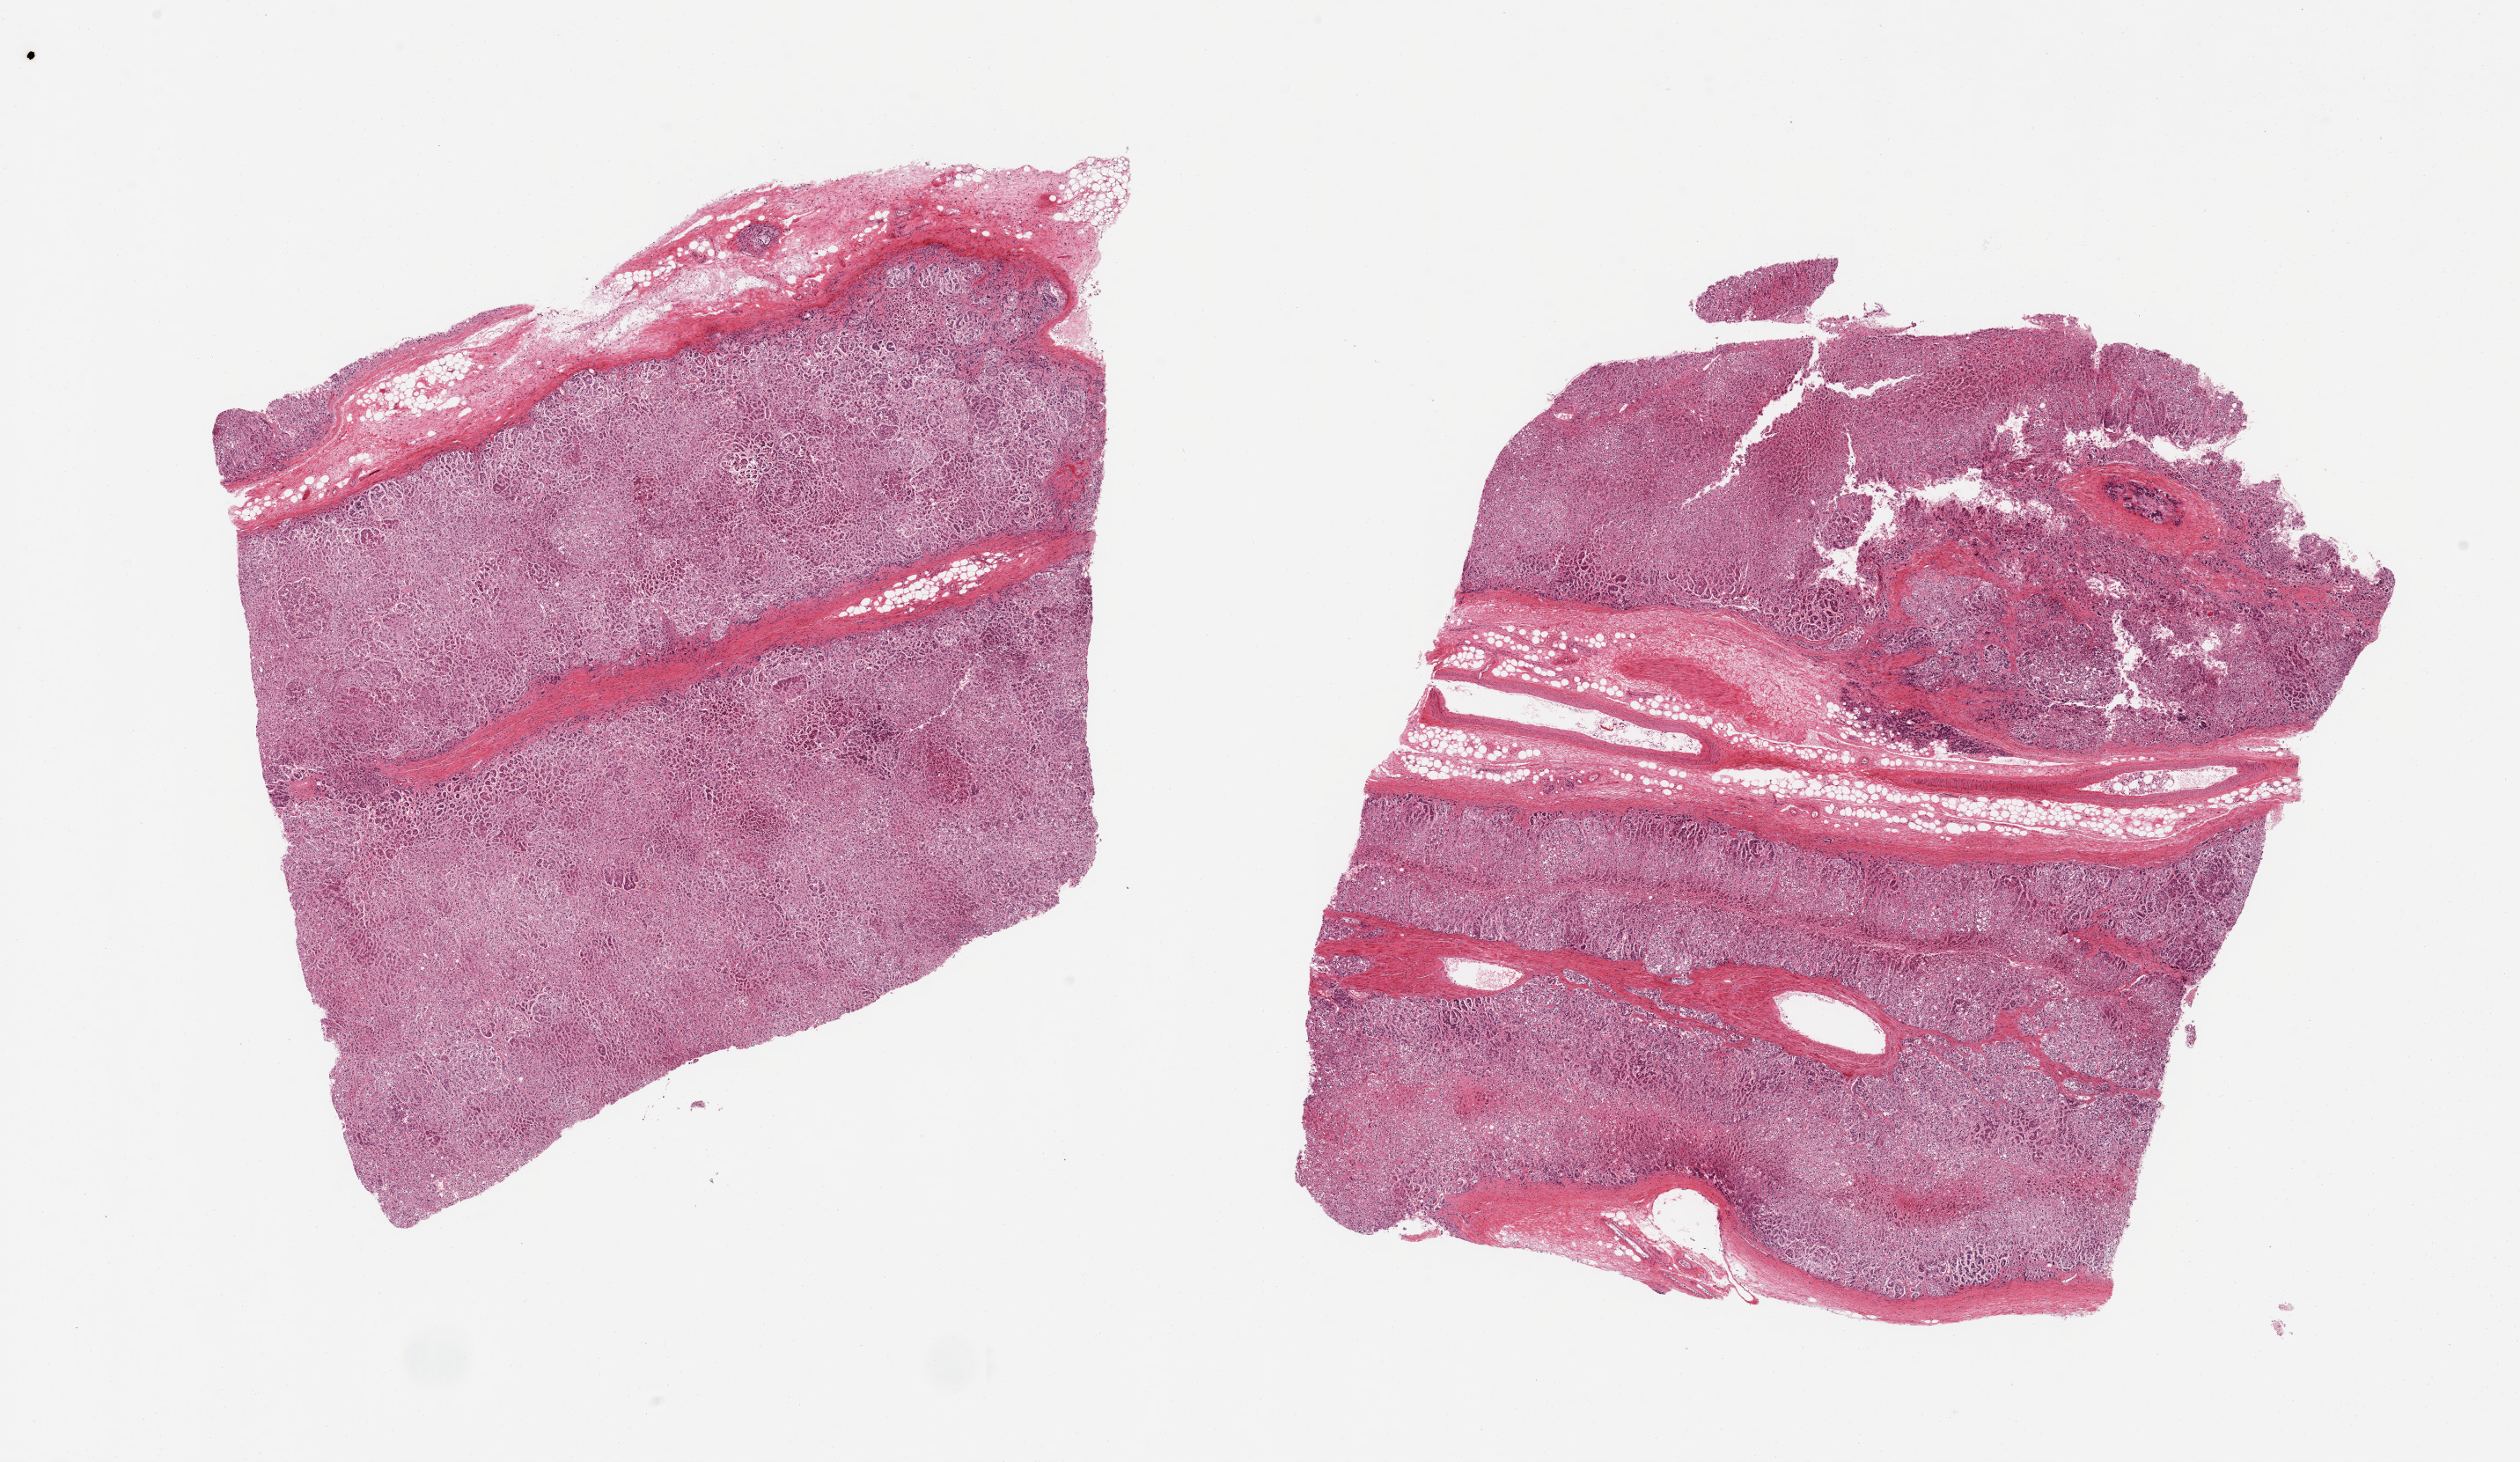
Digitized H&E-stained section — whole scanned area (about 22.6 x 13.1 mm, from a 20x scan) shown as a low-resolution overview, PAXgene-fixed paraffin-embedded (PFPE) section, section of adrenal gland (target tissue), tissue donor sample.
Pathologist's review note for this sample: 2 pieces; cortex with 10% fat.